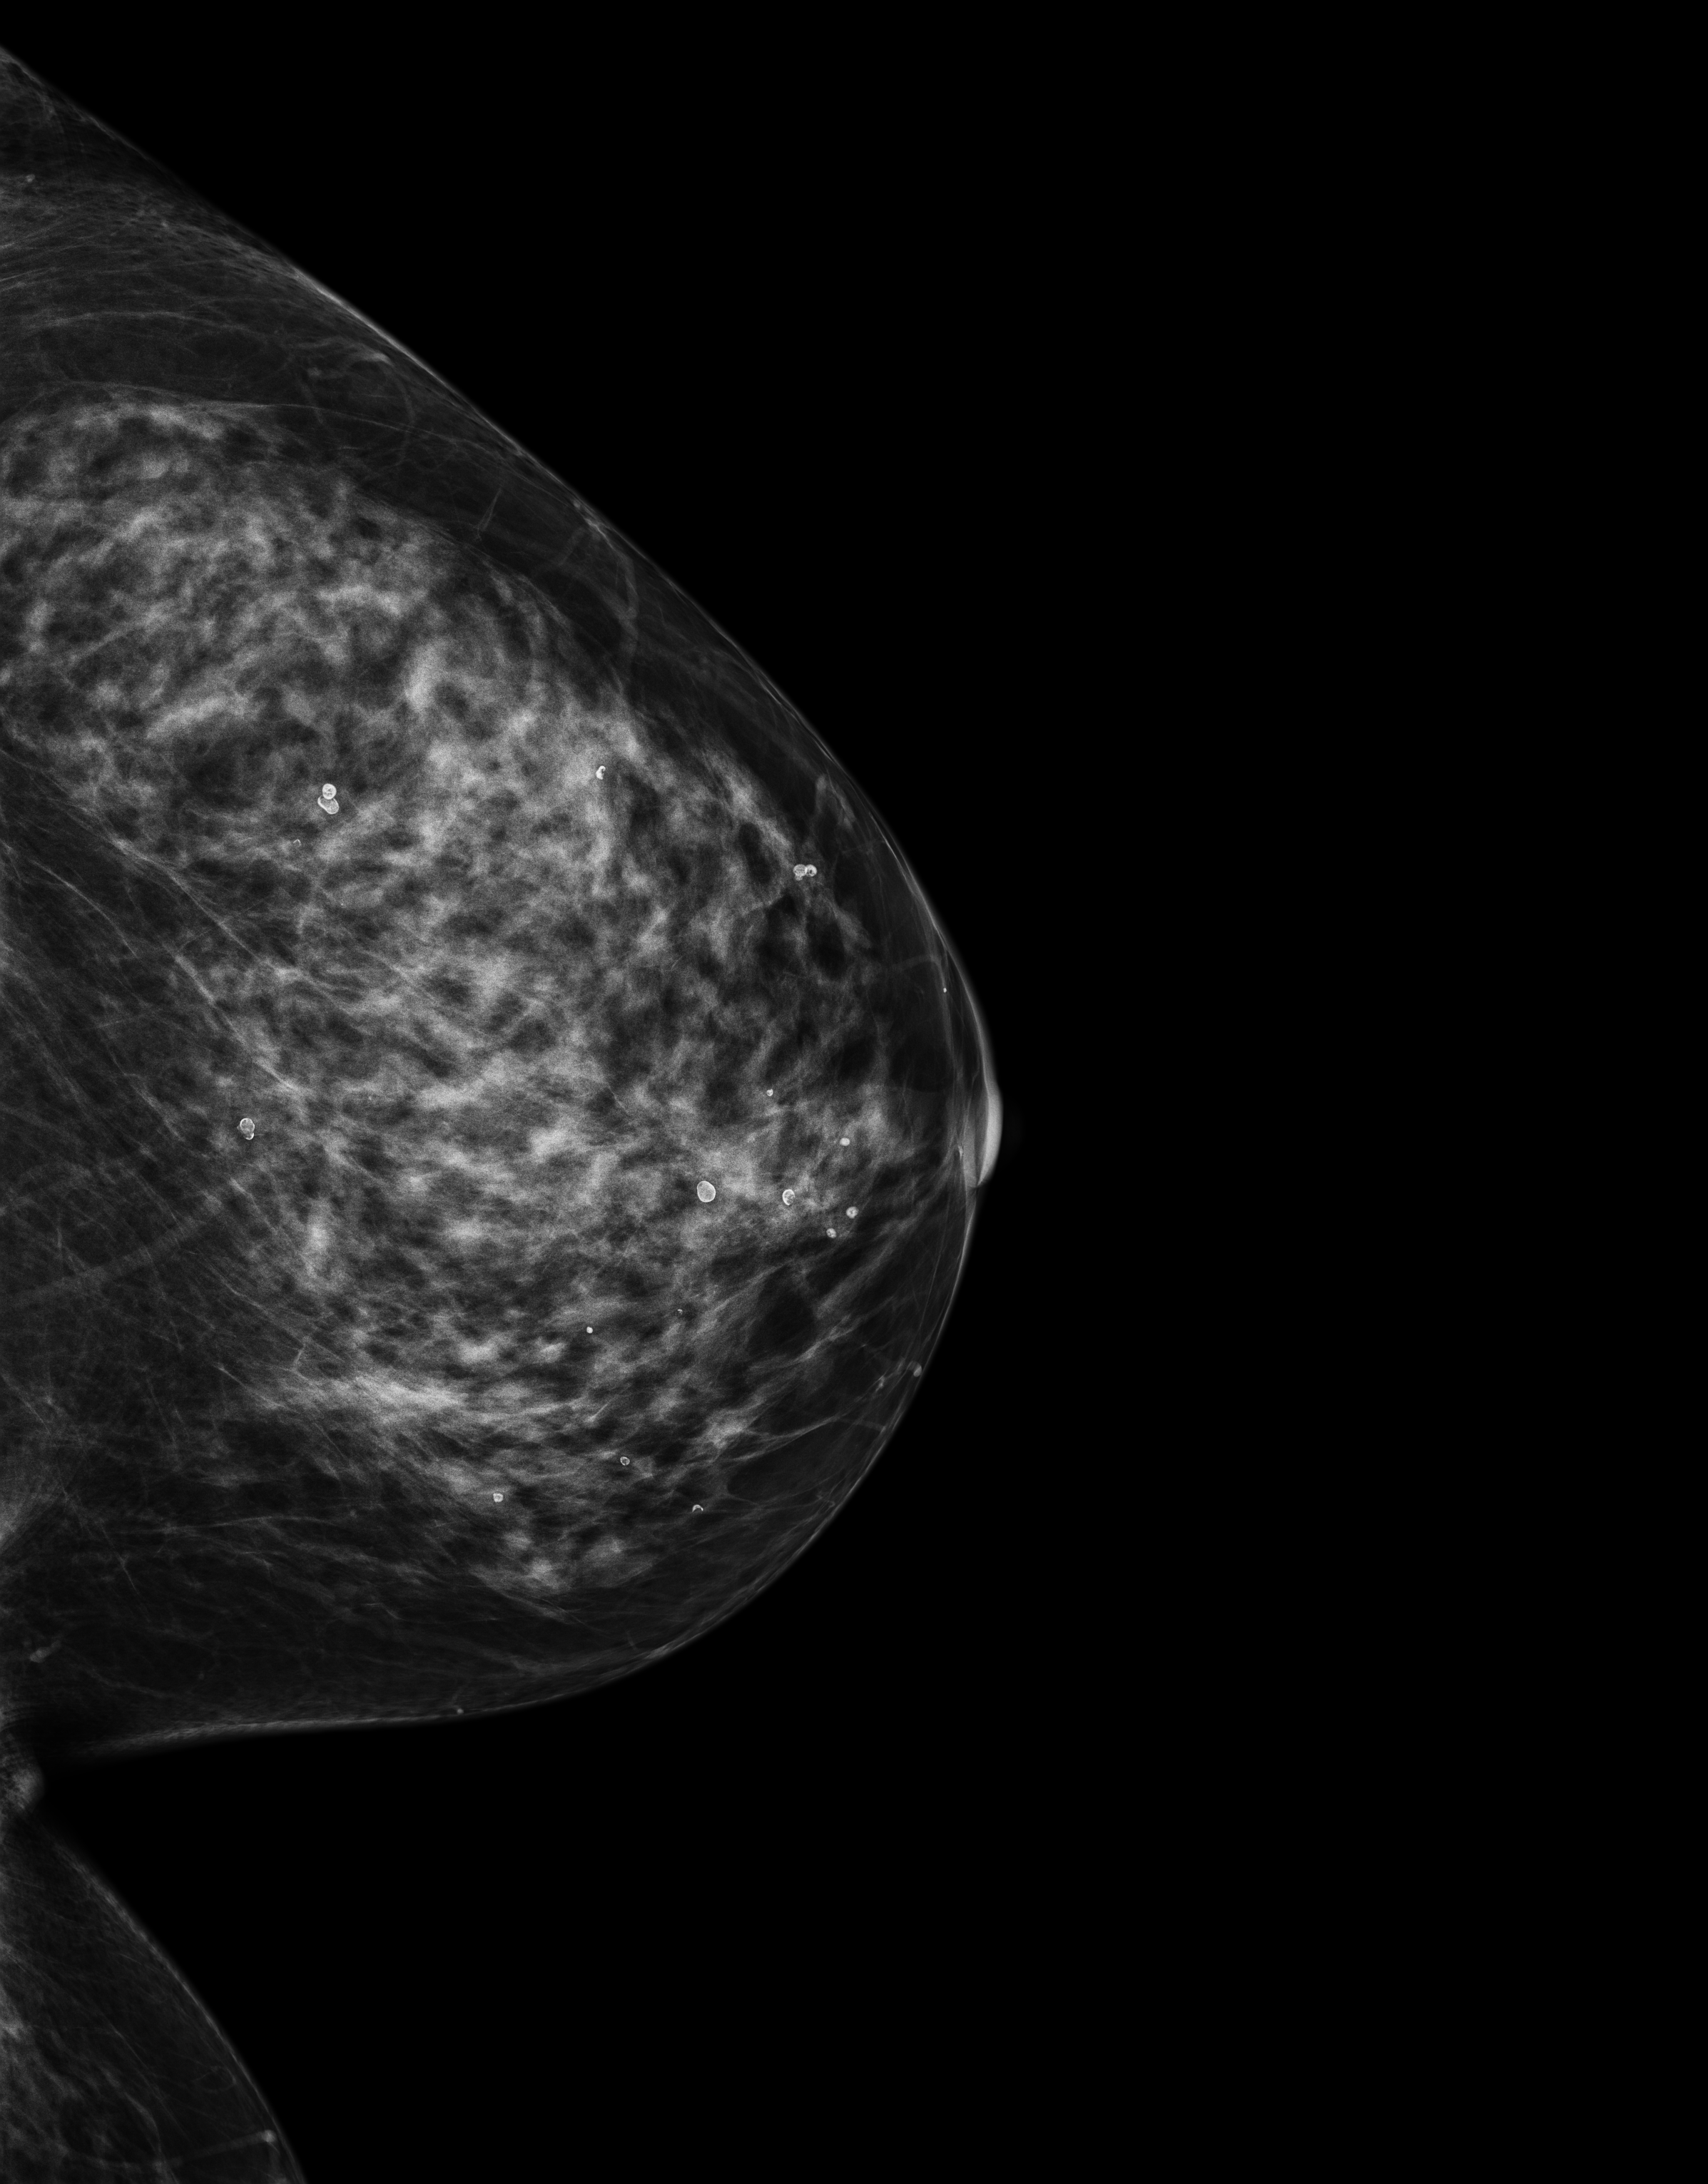
Annual screening mammography examination. Female patient, age 66 years.
Image type: full-field digital mammogram. Breast: left. Projection: CC view. BI-RADS breast density category at the screening exam (both breasts, scale 1–4): 3. Final BI-RADS assessment for this screening round (tomosynthesis exam, both breasts): category 1. Recall: no recall after this screen.